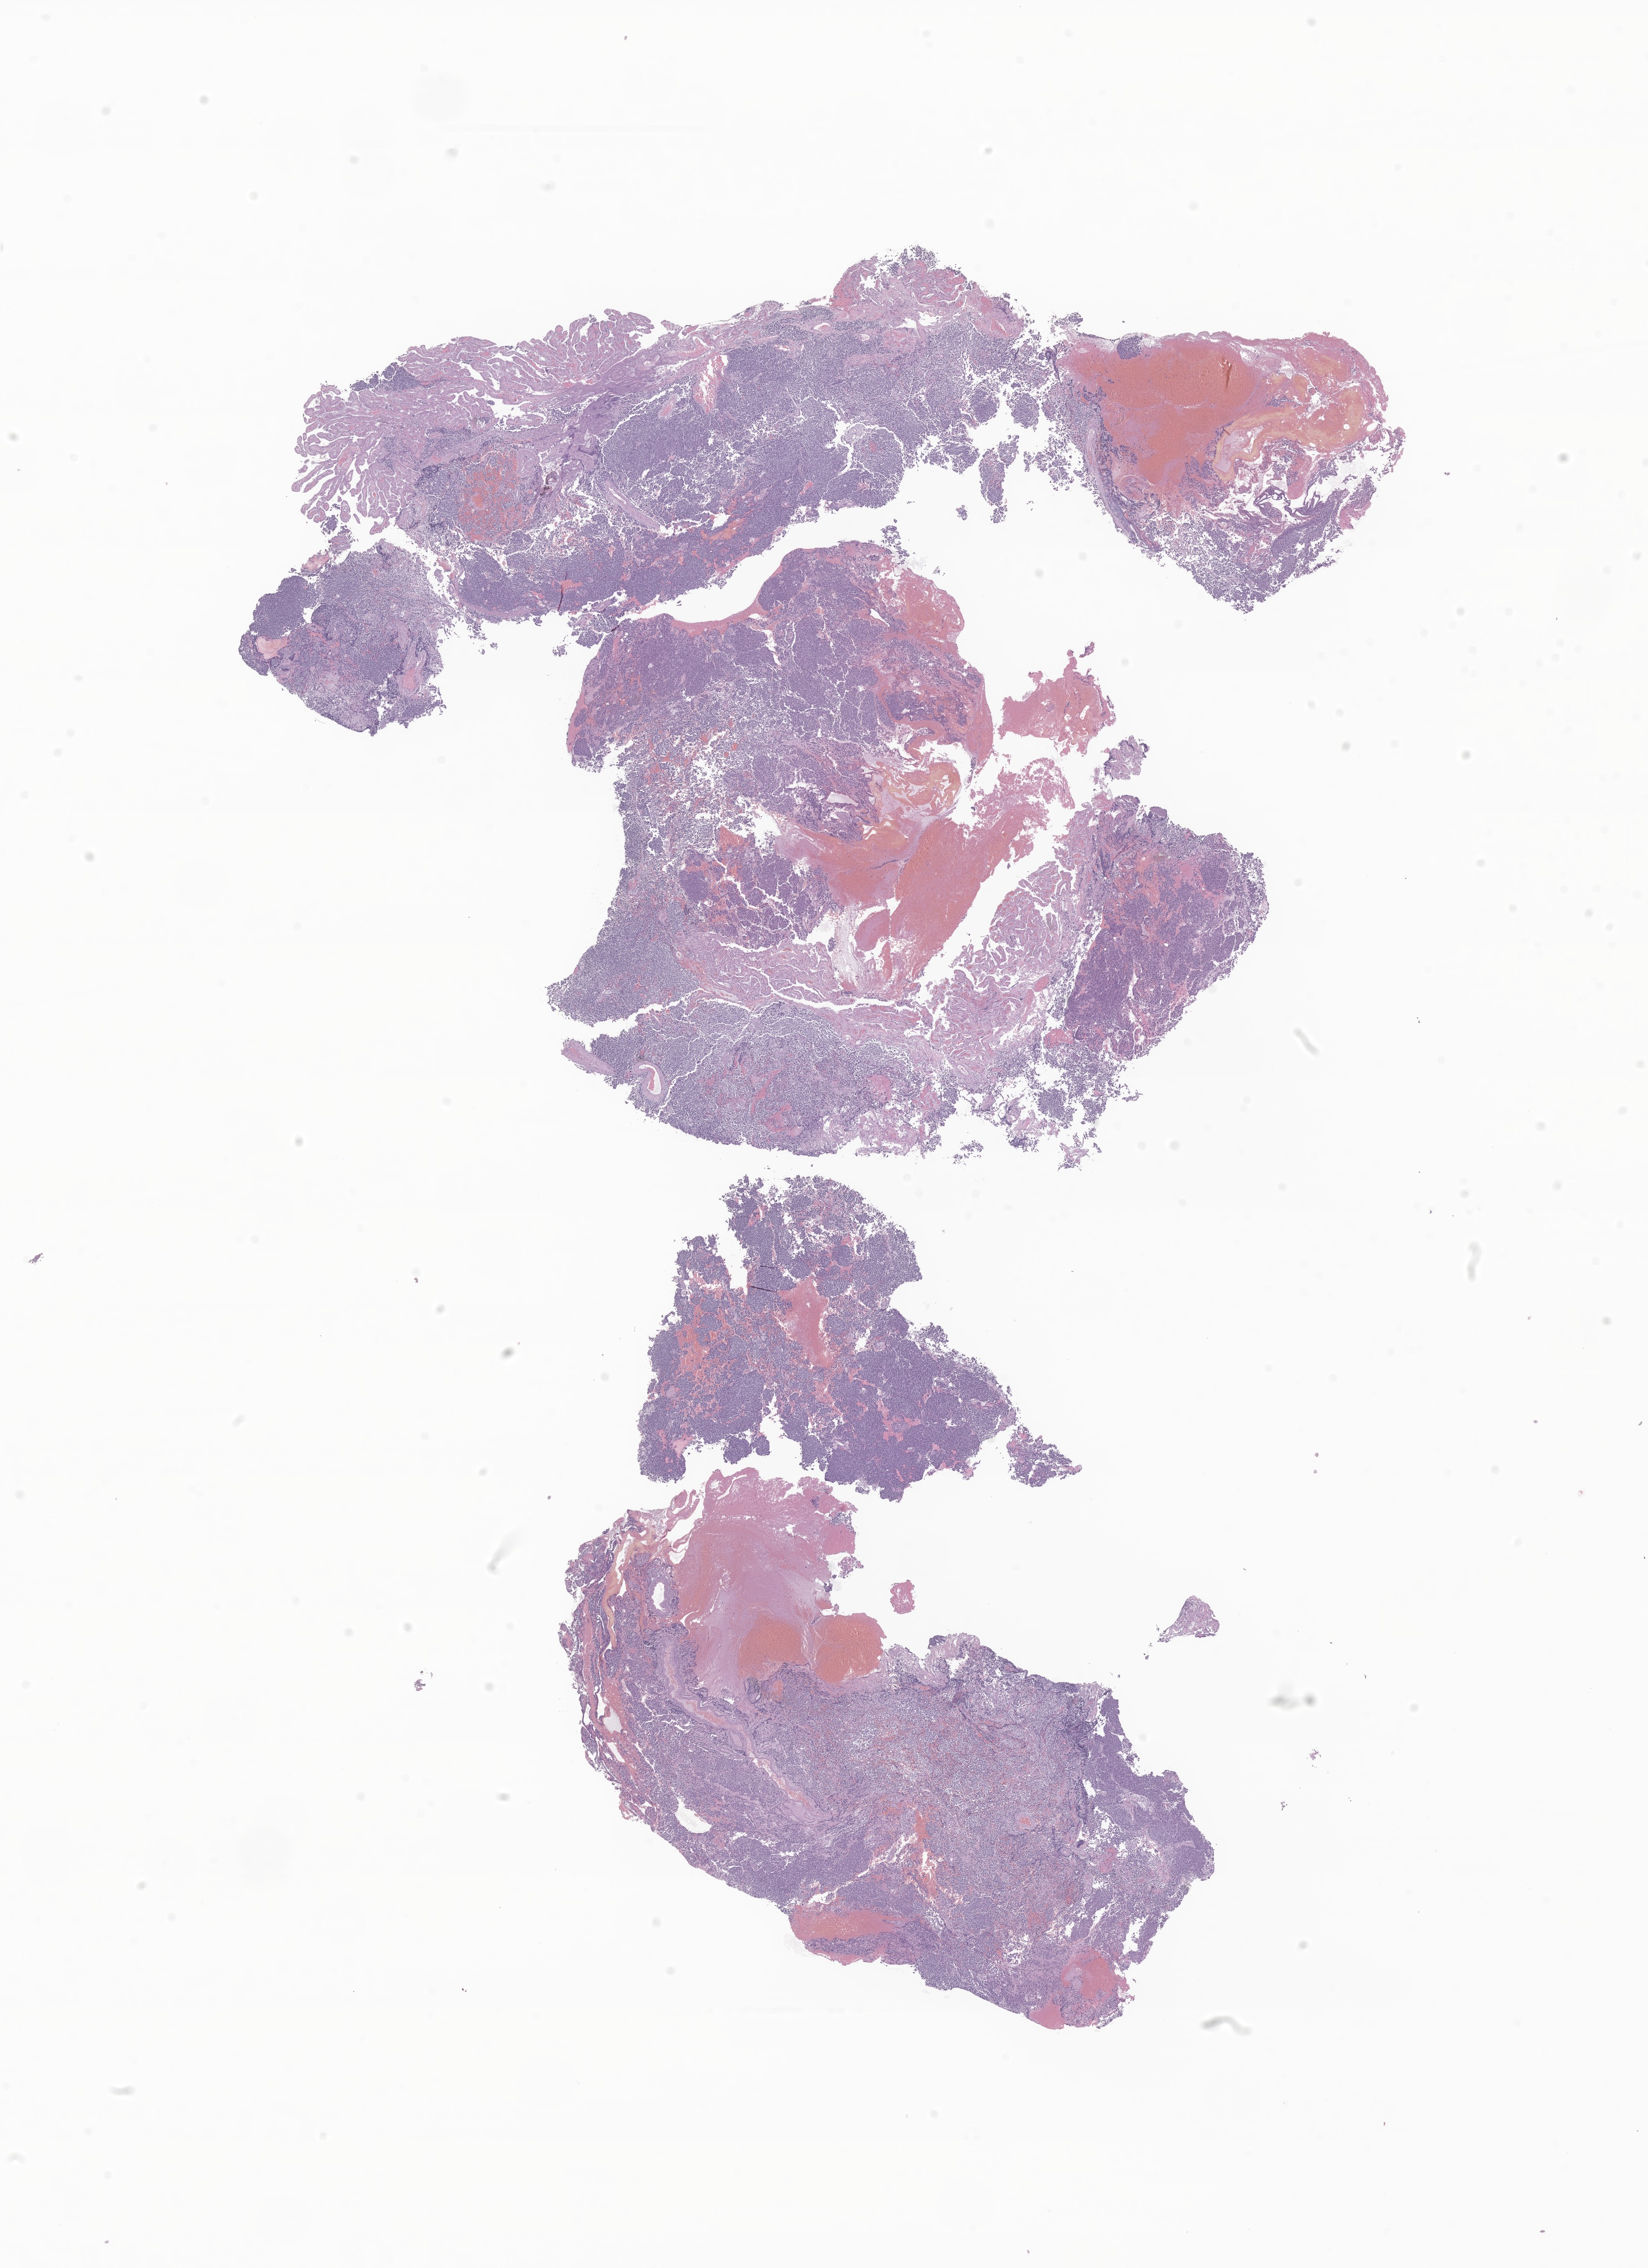
Hematoxylin and eosin (H&E) whole-slide image of tumor tissue from the brain, a low-resolution overview of the entire scanned area, about 13.3 x 18.2 mm; formalin-fixed, paraffin-embedded (FFPE) tissue. Patient female; age 126 months.
Recorded diagnosis: Medulloblastoma, NOS.